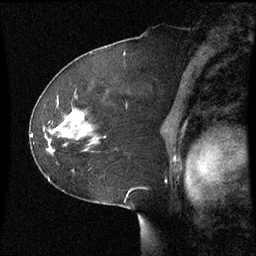
Breast MRI (dynamic contrast-enhanced), one sagittal slice. Dynamic contrast-enhanced series, image 2 of 3 at this slice position (ordered by acquisition). 1.5 T. TE 4.2 ms, TR 8.9 ms. 2.2 mm slice thickness. 256 × 256 image matrix. Female patient, age 51 years. From the clinical record (not read from this slice): setting: breast cancer imaged before/during neoadjuvant chemotherapy; receptor status: HR-positive, HER2-negative.
Structures marked on this image (semi-automatic segmentation, software-assisted and operator-edited):
- analysis volume of interest (the breast-tissue region the enhancement analysis was run in; not a lesion): box from (x=44, y=108) to (x=101, y=155) px
- tumour enhancement mask (voxels above the 70 % enhancement threshold inside the analysis volume of interest): (x=70, y=112)–(x=89, y=129)